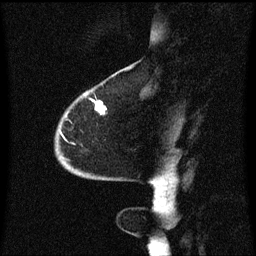
Breast MRI (dynamic contrast-enhanced), one sagittal slice; position 15 of 60 along the scan axis; dynamic contrast-enhanced series, image 2 of 3 at this slice position (ordered by acquisition); 1.5 T; TE 4.2 ms, TR 8.4 ms; 2 mm slice thickness; 256 × 256 image matrix, field of view 200 × 200 mm. Patient: female, 68 years. From the clinical record (not read from this slice): setting: breast cancer imaged before/during neoadjuvant chemotherapy; receptor status: triple-negative.
Outlined on this slice (semi-automatically segmented with operator editing):
- analysis volume of interest (the breast-tissue region the enhancement analysis was run in; not a lesion): bounding box (x1, y1, x2, y2) in pixels: (56, 94, 108, 173)
- tumour enhancement mask (voxels above the 70 % enhancement threshold inside the analysis volume of interest): (96, 102, 107, 115)